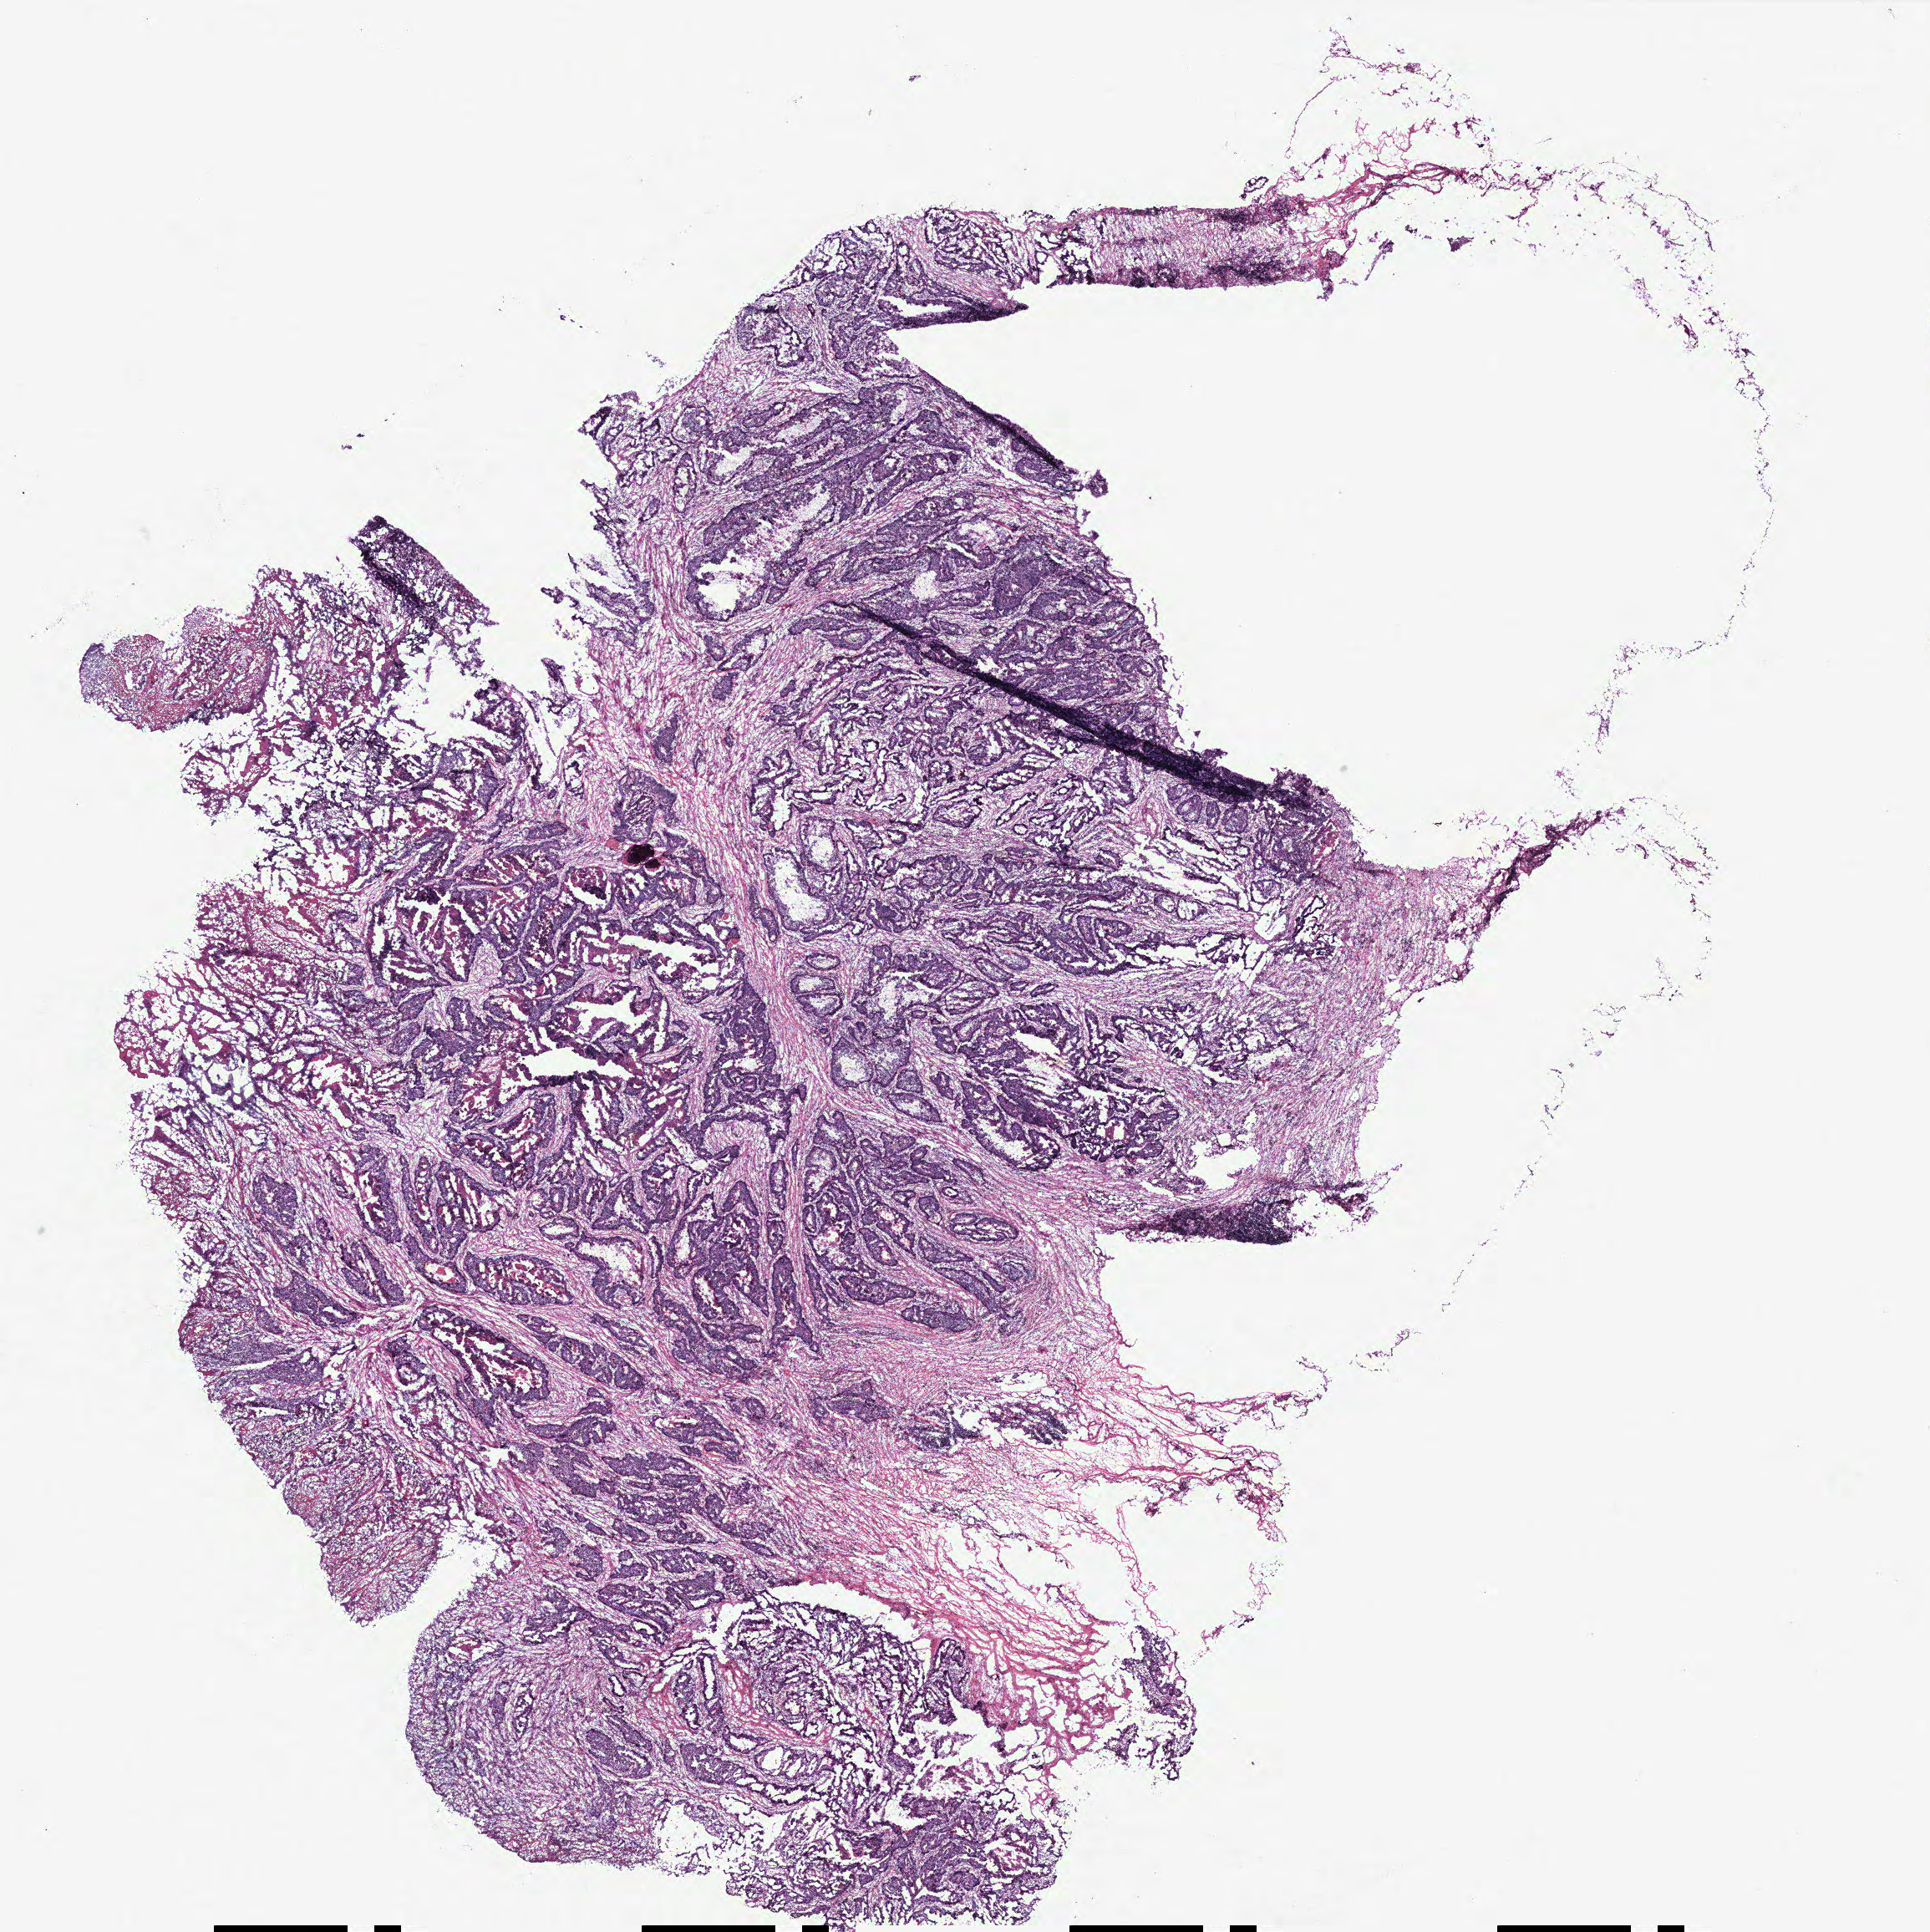
Digitized H&E-stained tissue section (whole slide) — a low-resolution overview of the entire scanned area, about 18.5 x 18.5 mm (acquisition: 40x scan). Tumour tissue sample, colon. 69-year-old female patient.
* primary tumour site (as recorded): colon
* histologic diagnosis: Adenocarcinoma, NOS
* AJCC pathologic stage: IVA